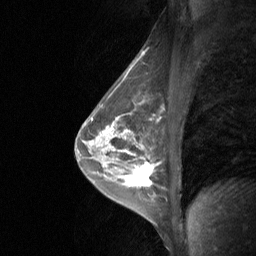
Breast MRI (dynamic contrast-enhanced), one sagittal slice; slice 42 of 64 in the series (ordered by position); dynamic contrast-enhanced study with each time point stored as its own series, time point 2 of 3 at this slice position (early post-contrast, ordered by acquisition time); 1.5 T; TE 4.8 ms, TR 27 ms; 256 × 256 image matrix. Patient: female, 47 years. Case-level facts recorded for this patient, not image findings: setting: breast cancer imaged before/during neoadjuvant chemotherapy; receptor status: HR-positive, HER2-negative.
Annotated regions visible in this slice (semi-automatically segmented with operator editing):
- analysis volume of interest (the breast-tissue region the enhancement analysis was run in; not a lesion): bounding box (x1, y1, x2, y2) in pixels: (120, 161, 151, 203)
- tumour enhancement mask (voxels above the 90 % enhancement threshold inside the analysis volume of interest): (137, 168, 148, 185)